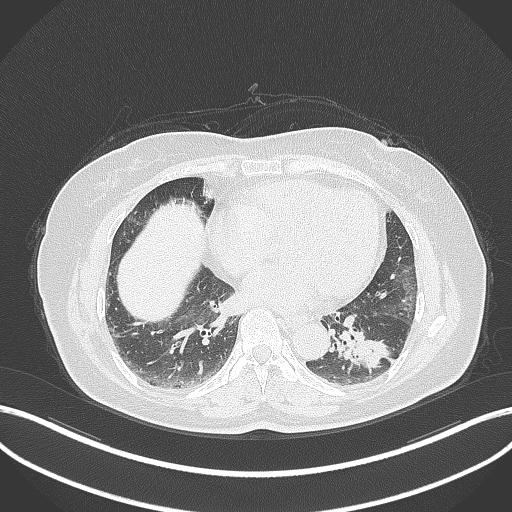
Chest CT, one axial slice; position 146 of 311 along the scan axis; lung window (W 1500 / L -600 HU); 1 mm slice thickness; 512 × 512 image matrix, field of view 400 × 400 mm. Female patient, age 59 years. Case-level facts recorded for this patient, not image findings: clinical TNM (as recorded): T2a N0 M0.
Outlined on this slice (bounding box drawn by a radiologist):
- lung tumour (recorded histology: adenocarcinoma): bounding box (x1, y1, x2, y2) in pixels: (327, 328, 388, 375)